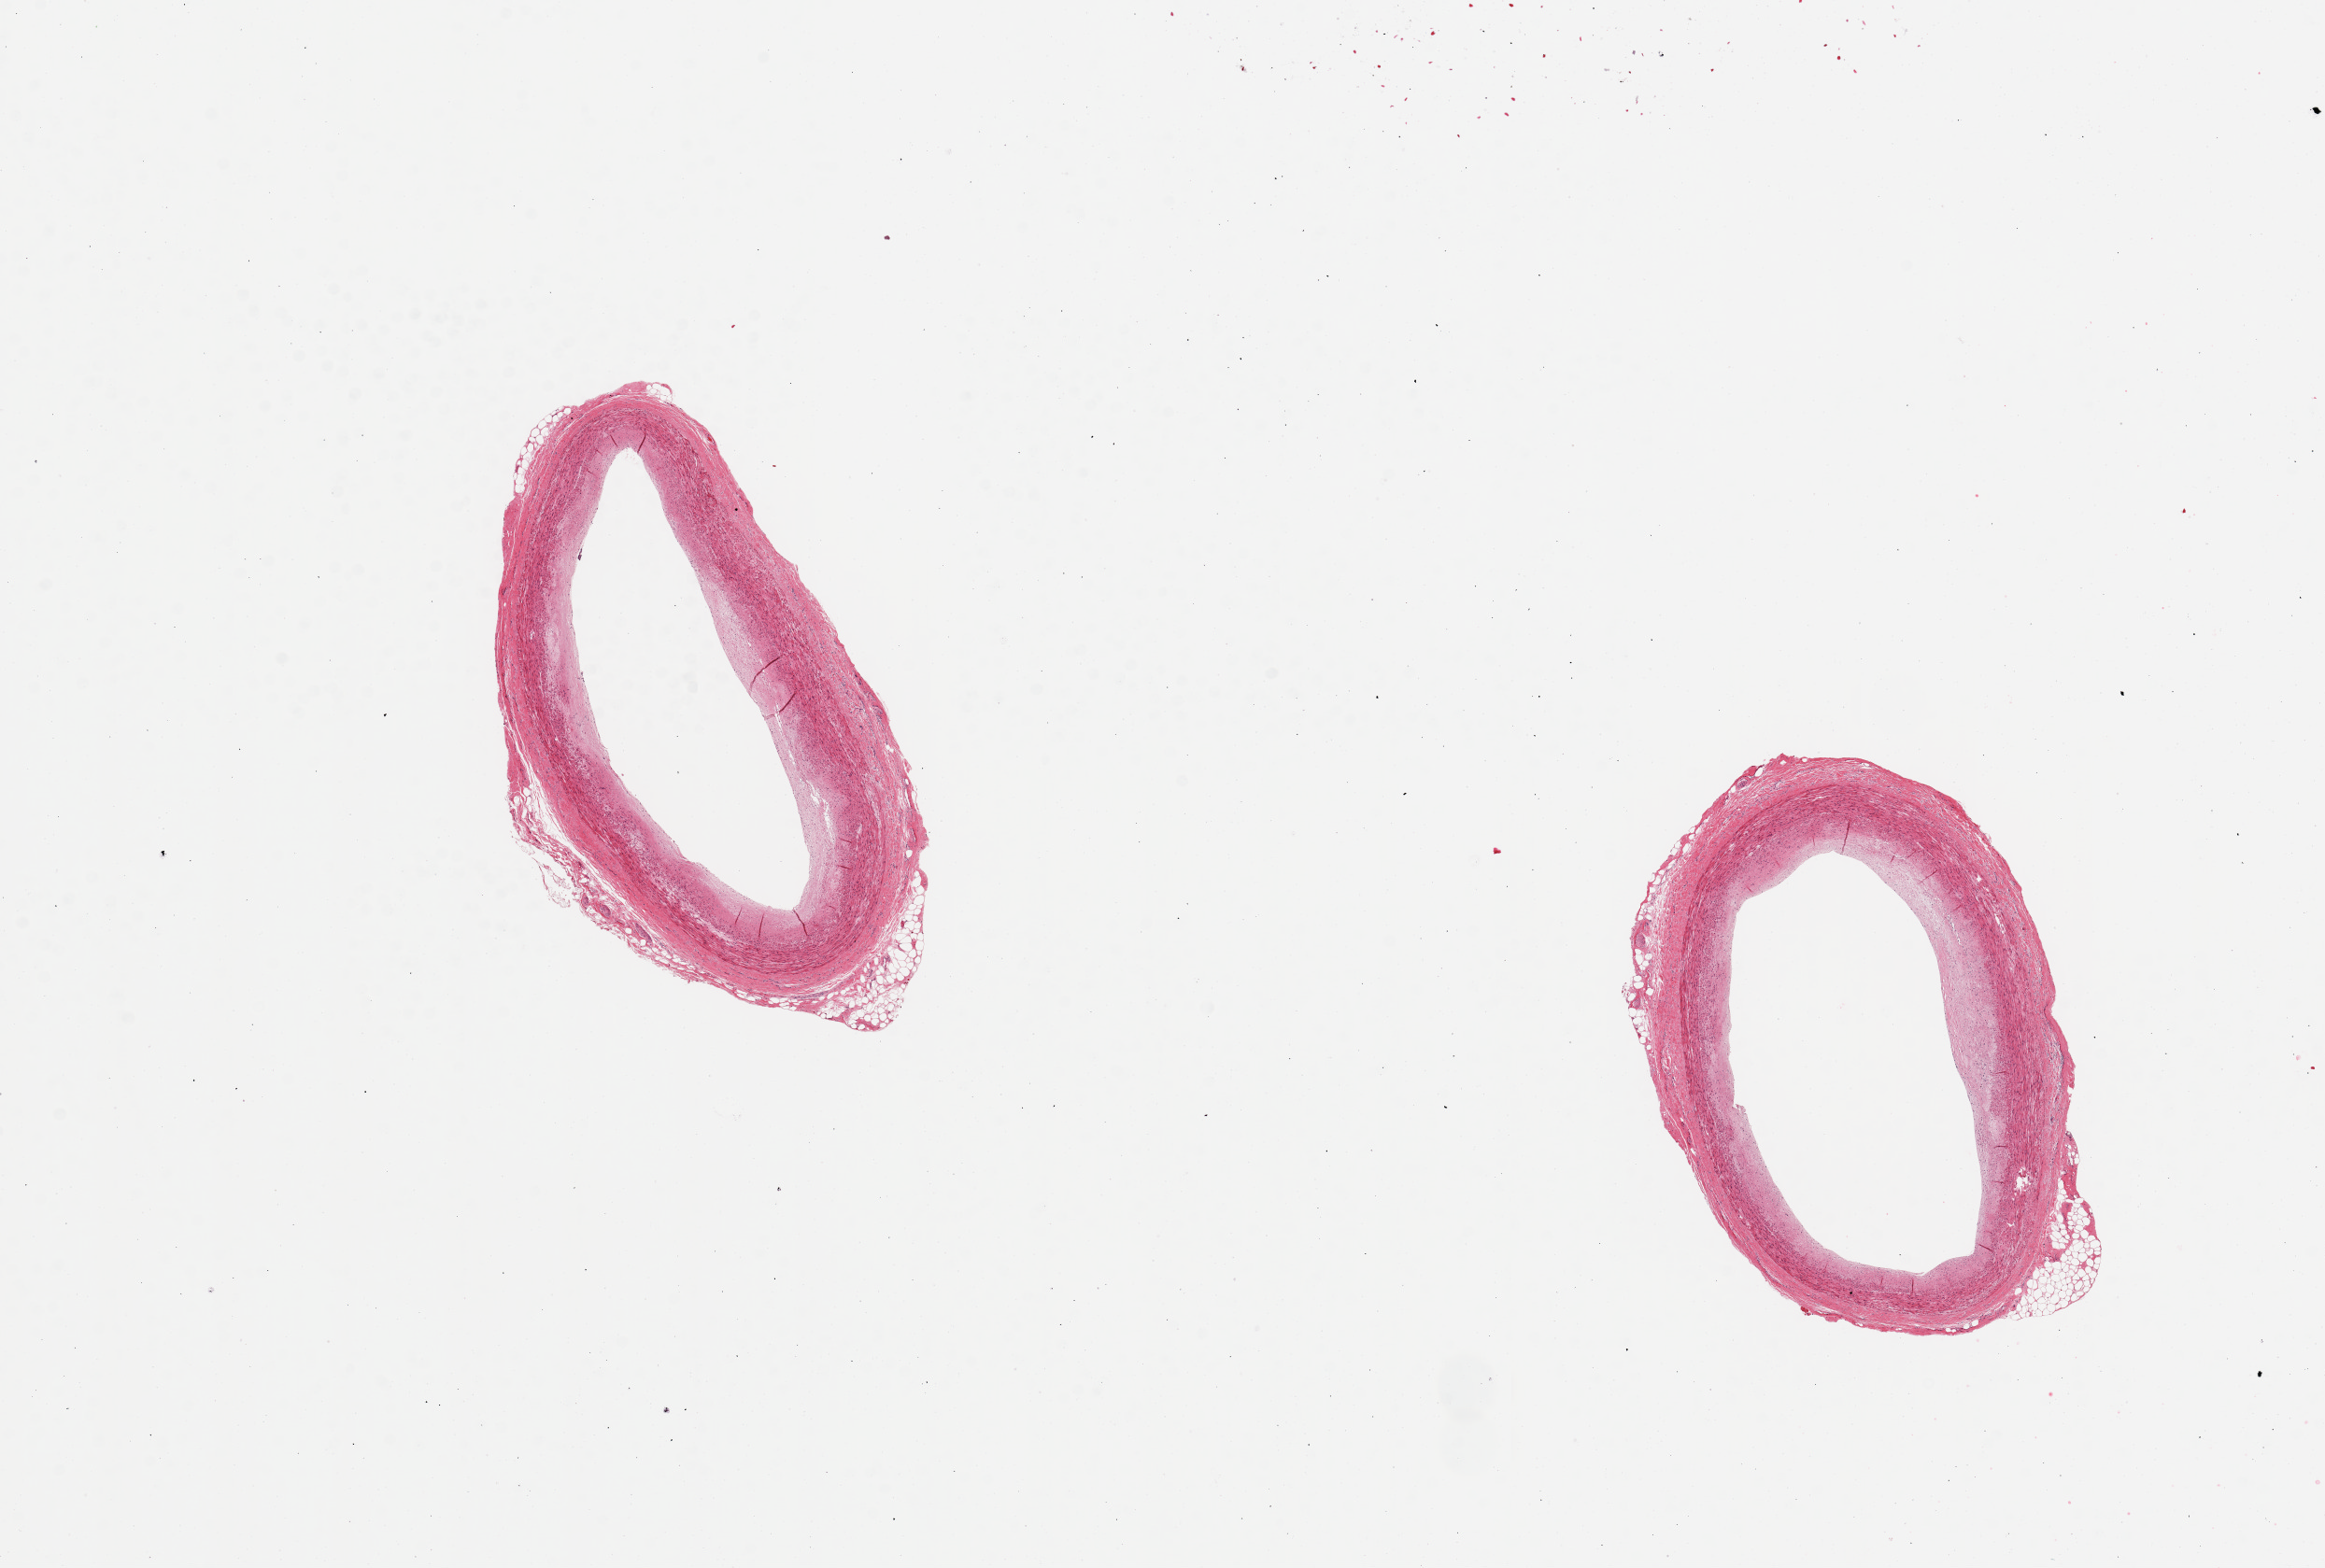
Haematoxylin and eosin whole-slide image, brightfield — low-resolution overview of the scanned area, about 19.7 x 13.3 mm (slide scanned at 20x), PAXgene-fixed, paraffin-embedded tissue, target tissue: coronary artery, tissue donor sample. Male donor.
• reviewer comment on this tissue sample: 2 pieces, minimal atherosis, ~10% occlusion